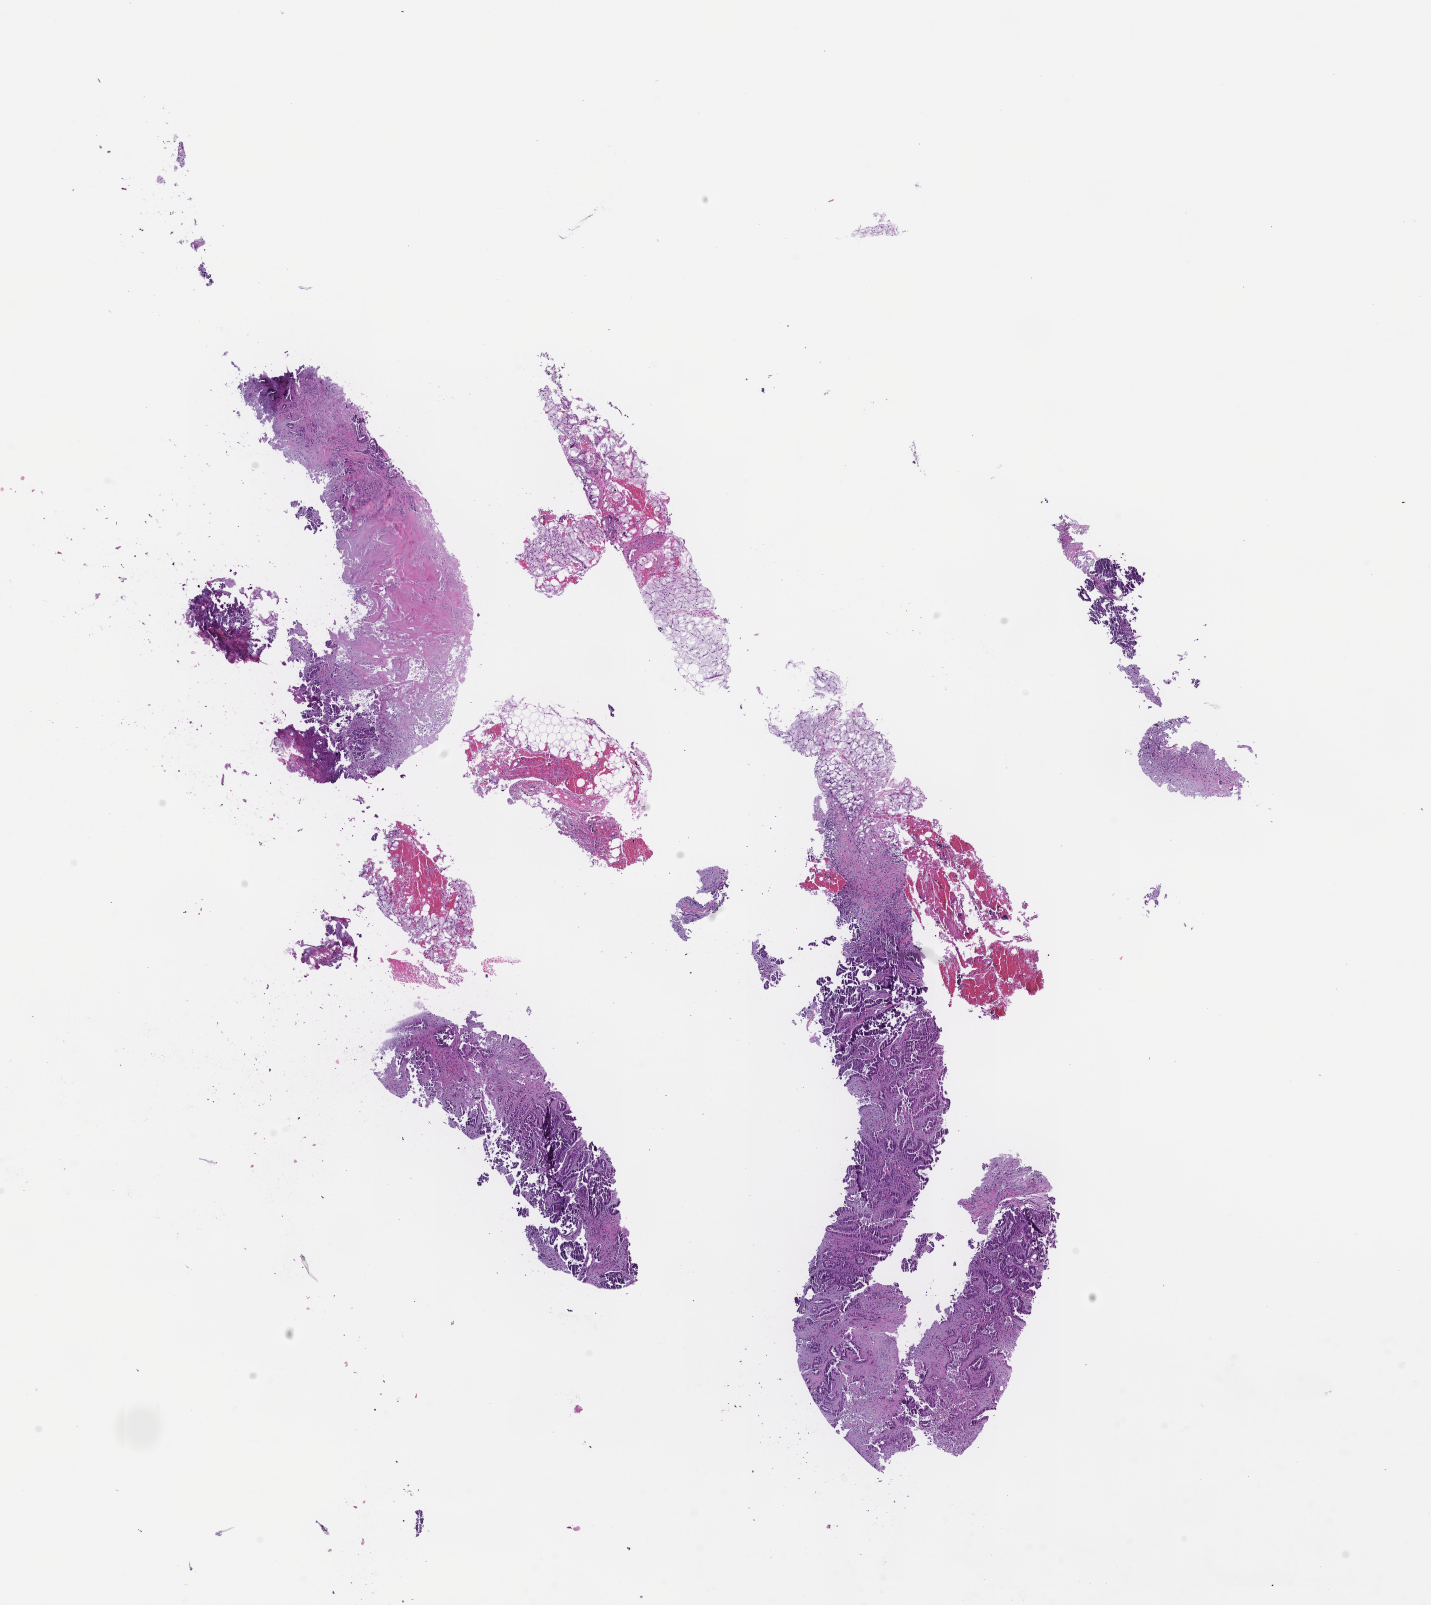
Whole-slide image, haematoxylin and eosin stain, whole scanned area (about 11.6 x 13.0 mm) shown as a low-resolution overview; formalin-fixed, paraffin-embedded (FFPE) tissue; archival tissue. Female patient.
This section: metastatic tumor tissue. Primary diagnosis of the patient: Non-Small Cell Lung Carcinoma.